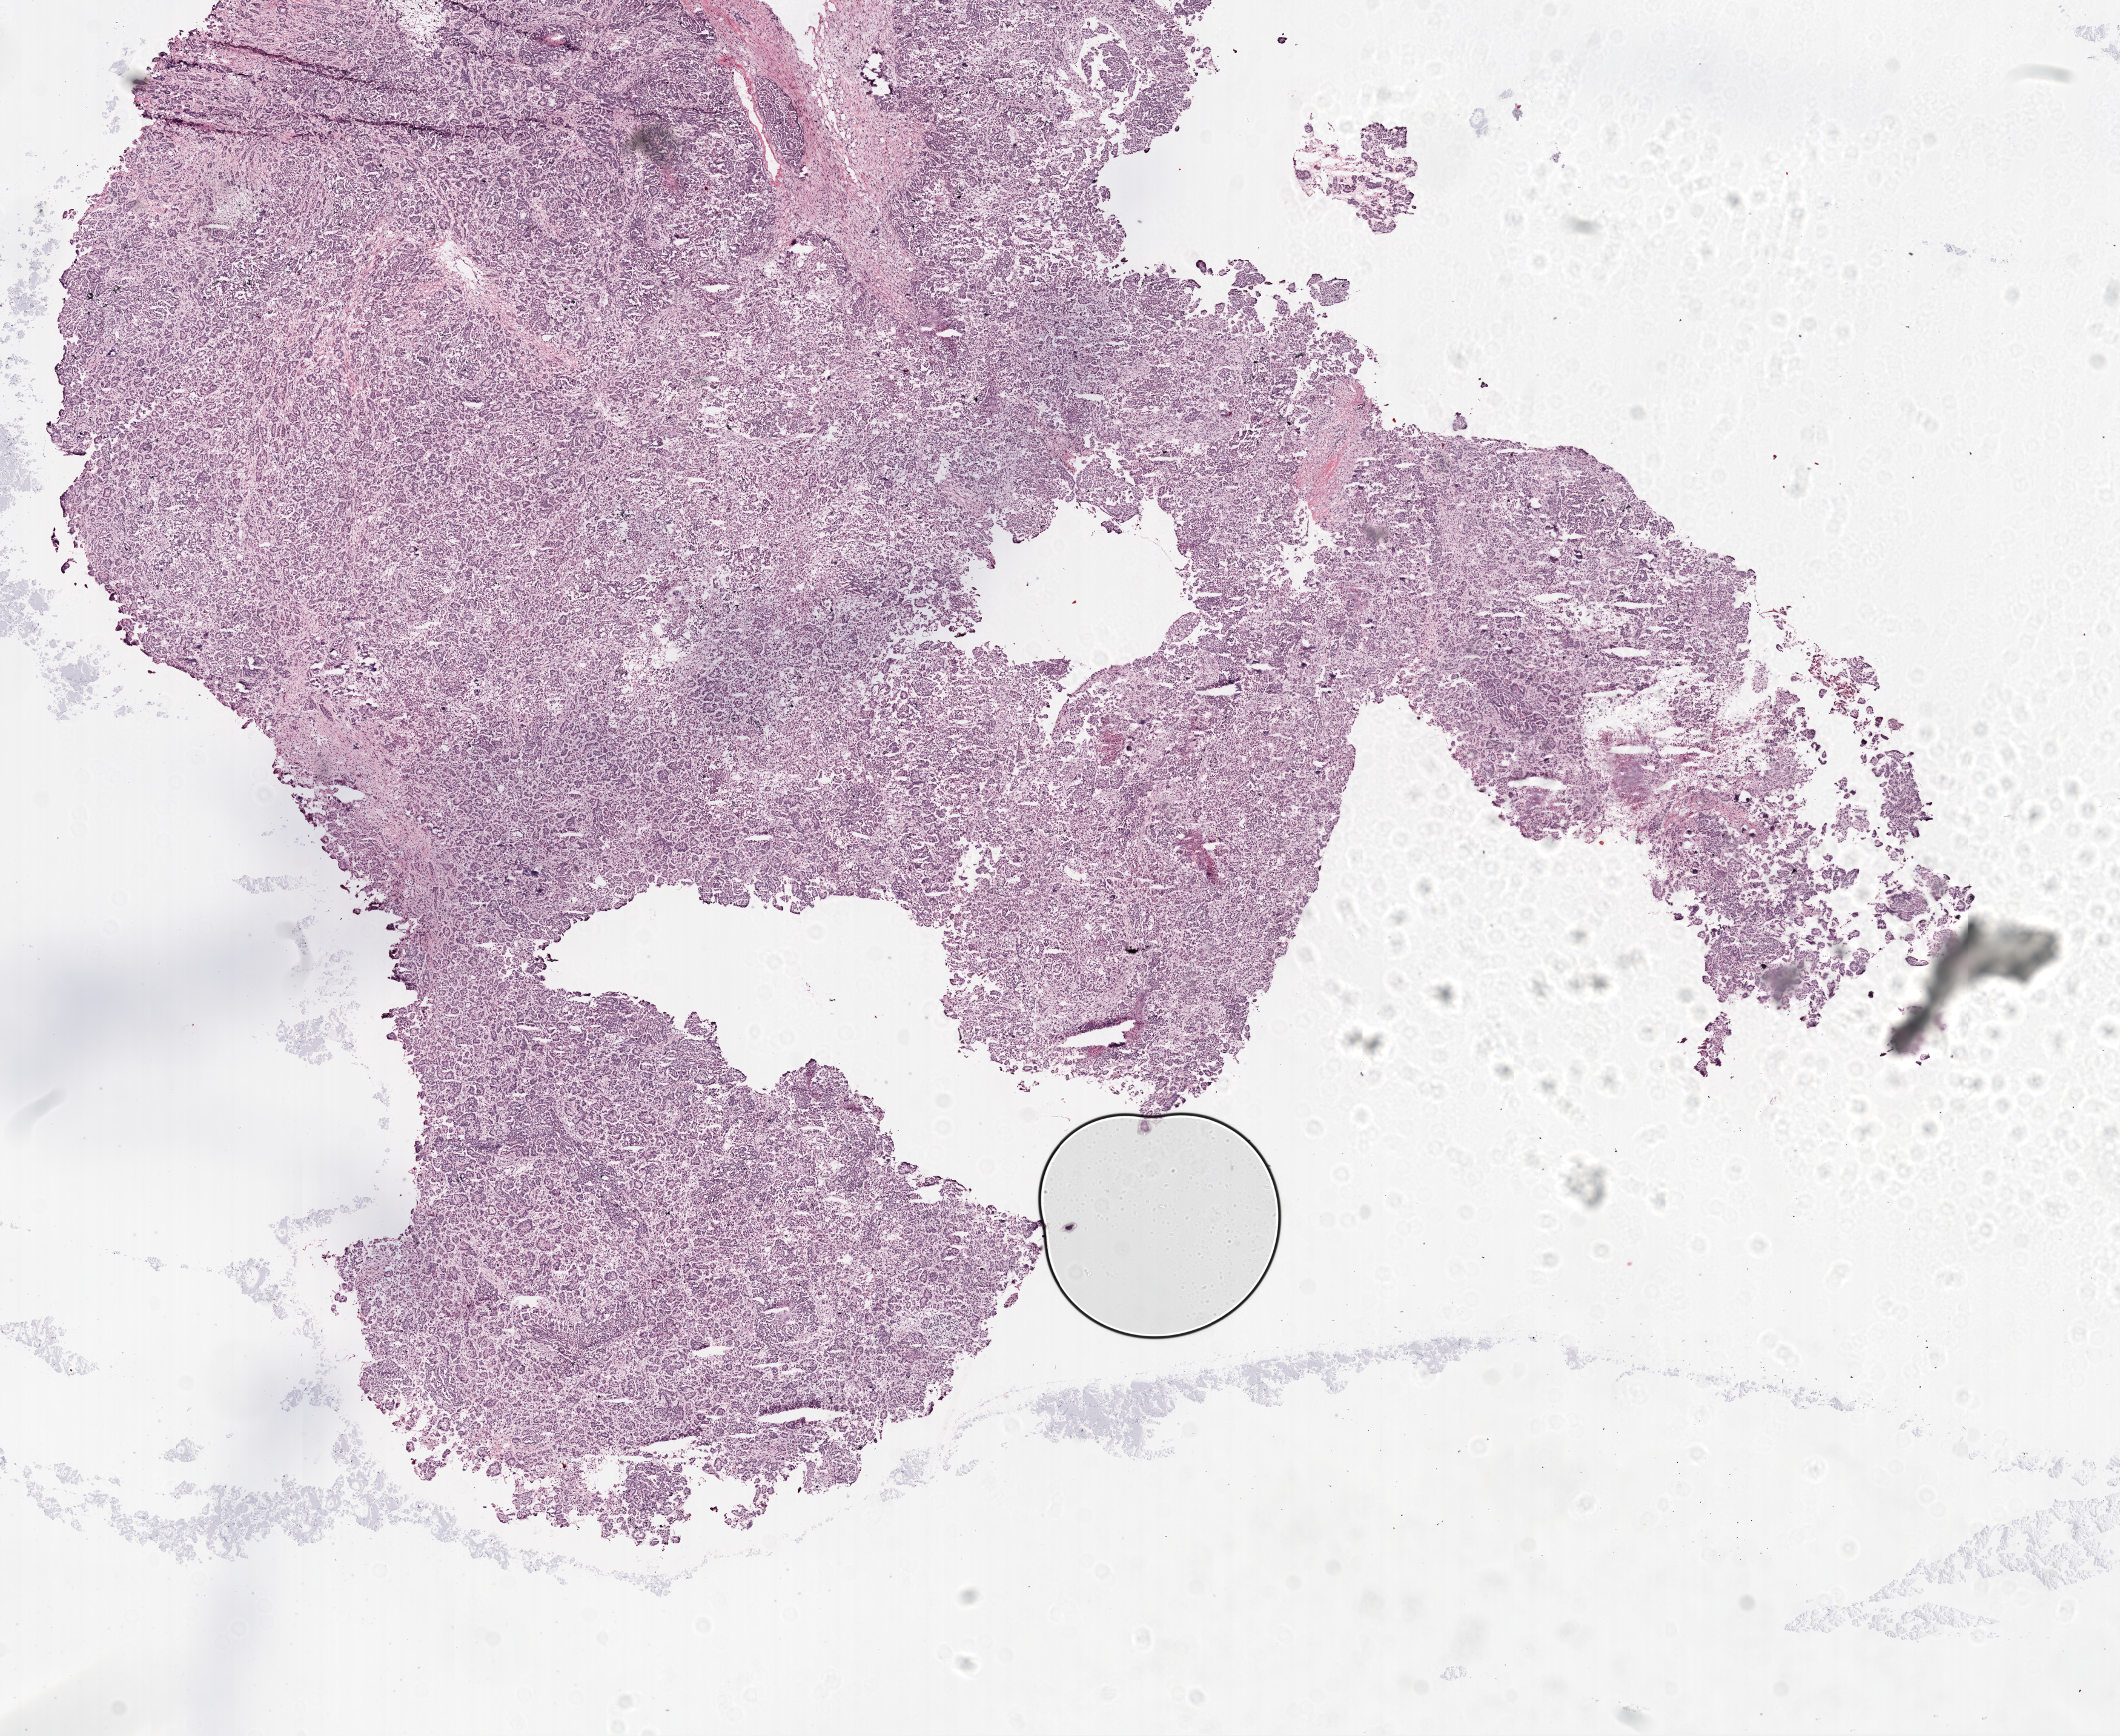
H&E whole-slide image, whole scanned area (about 14.0 x 11.5 mm, from a 20x scan) shown as a low-resolution overview; frozen section from the top of the tissue portion; sample: primary tumour, ovary. Female patient; age at initial diagnosis 36 years. Histologic grade: G2 (moderately differentiated). Composition of this section per pathologist review: tumour cells 95%, tumour nuclei 99%, normal cells 0%, stromal cells 5%, necrosis 0%.
- diagnosis: Serous cystadenocarcinoma, NOS
- FIGO stage: IIIC
- laterality: bilateral